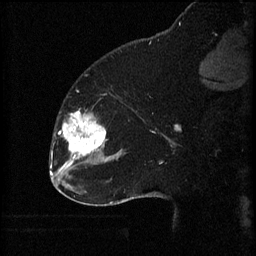
Breast MRI (dynamic contrast-enhanced), one sagittal slice. Slice 20 of 60 in the series (ordered by position). 3 images stored at this slice position (order not interpretable as contrast timing). 1.5 T. TE 4.2 ms, TR 8.2 ms. 2 mm slice thickness. 256 × 256 image matrix, field of view 180 × 180 mm. Female patient, age 32 years.
Annotated regions visible in this slice (semi-automatic segmentation, software-assisted and operator-edited):
- analysis volume of interest (the breast-tissue region the enhancement analysis was run in; not a lesion): bounding box [x1, y1, x2, y2] px = [58, 110, 111, 165]
- tumour enhancement mask (voxels above the 70 % enhancement threshold inside the analysis volume of interest): [63, 110, 106, 165]